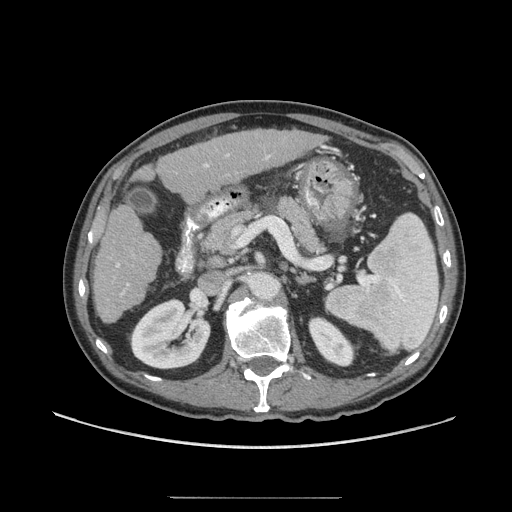
Contrast-enhanced abdominal CT (liver protocol), one axial slice; position 29 of 71 along the scan axis; soft-tissue window (W 400 / L 40 HU); 2.5 mm slice thickness; 512 × 512 image matrix, field of view 400 × 400 mm. From the clinical record (not read from this slice): diagnosis: hepatocellular carcinoma (patient treated with transarterial chemoembolisation; whether this scan precedes or follows treatment is not stated here); TNM stage (as recorded): Stage-I; Child-Pugh class: A; tumour differentiation: well differentiated; tumour nodularity: uninodular.
Annotated regions visible in this slice (semi-automatically segmented with operator editing):
- liver parenchyma outside the tumour (the mass and vessels are separate outlines, so this box may not span the whole liver): bounding box <92,130,320,322> (left, top, right, bottom; pixels)
- liver vessels: <116,154,270,295>